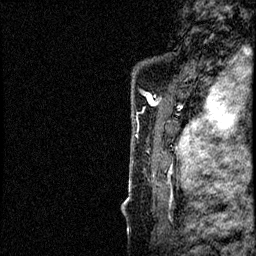
Breast MRI (dynamic contrast-enhanced), one sagittal slice; dynamic contrast-enhanced study with each time point stored as its own series, time point 2 of 4 at this slice position (early post-contrast, ordered by acquisition time); 1.5 T; TE 4.2 ms, TR 17.6 ms; 2 mm slice thickness; 256 × 256 image matrix. Patient: female, 40 years. From the clinical record (not read from this slice): setting: breast cancer imaged before/during neoadjuvant chemotherapy; receptor status: HER2-positive.
Structures marked on this image (semi-automatically segmented with operator editing):
- analysis volume of interest (the breast-tissue region the enhancement analysis was run in; not a lesion): bounding box [x1, y1, x2, y2] px = [124, 56, 197, 205]
- tumour enhancement mask (voxels above the 100 % enhancement threshold inside the analysis volume of interest): [129, 131, 196, 189]